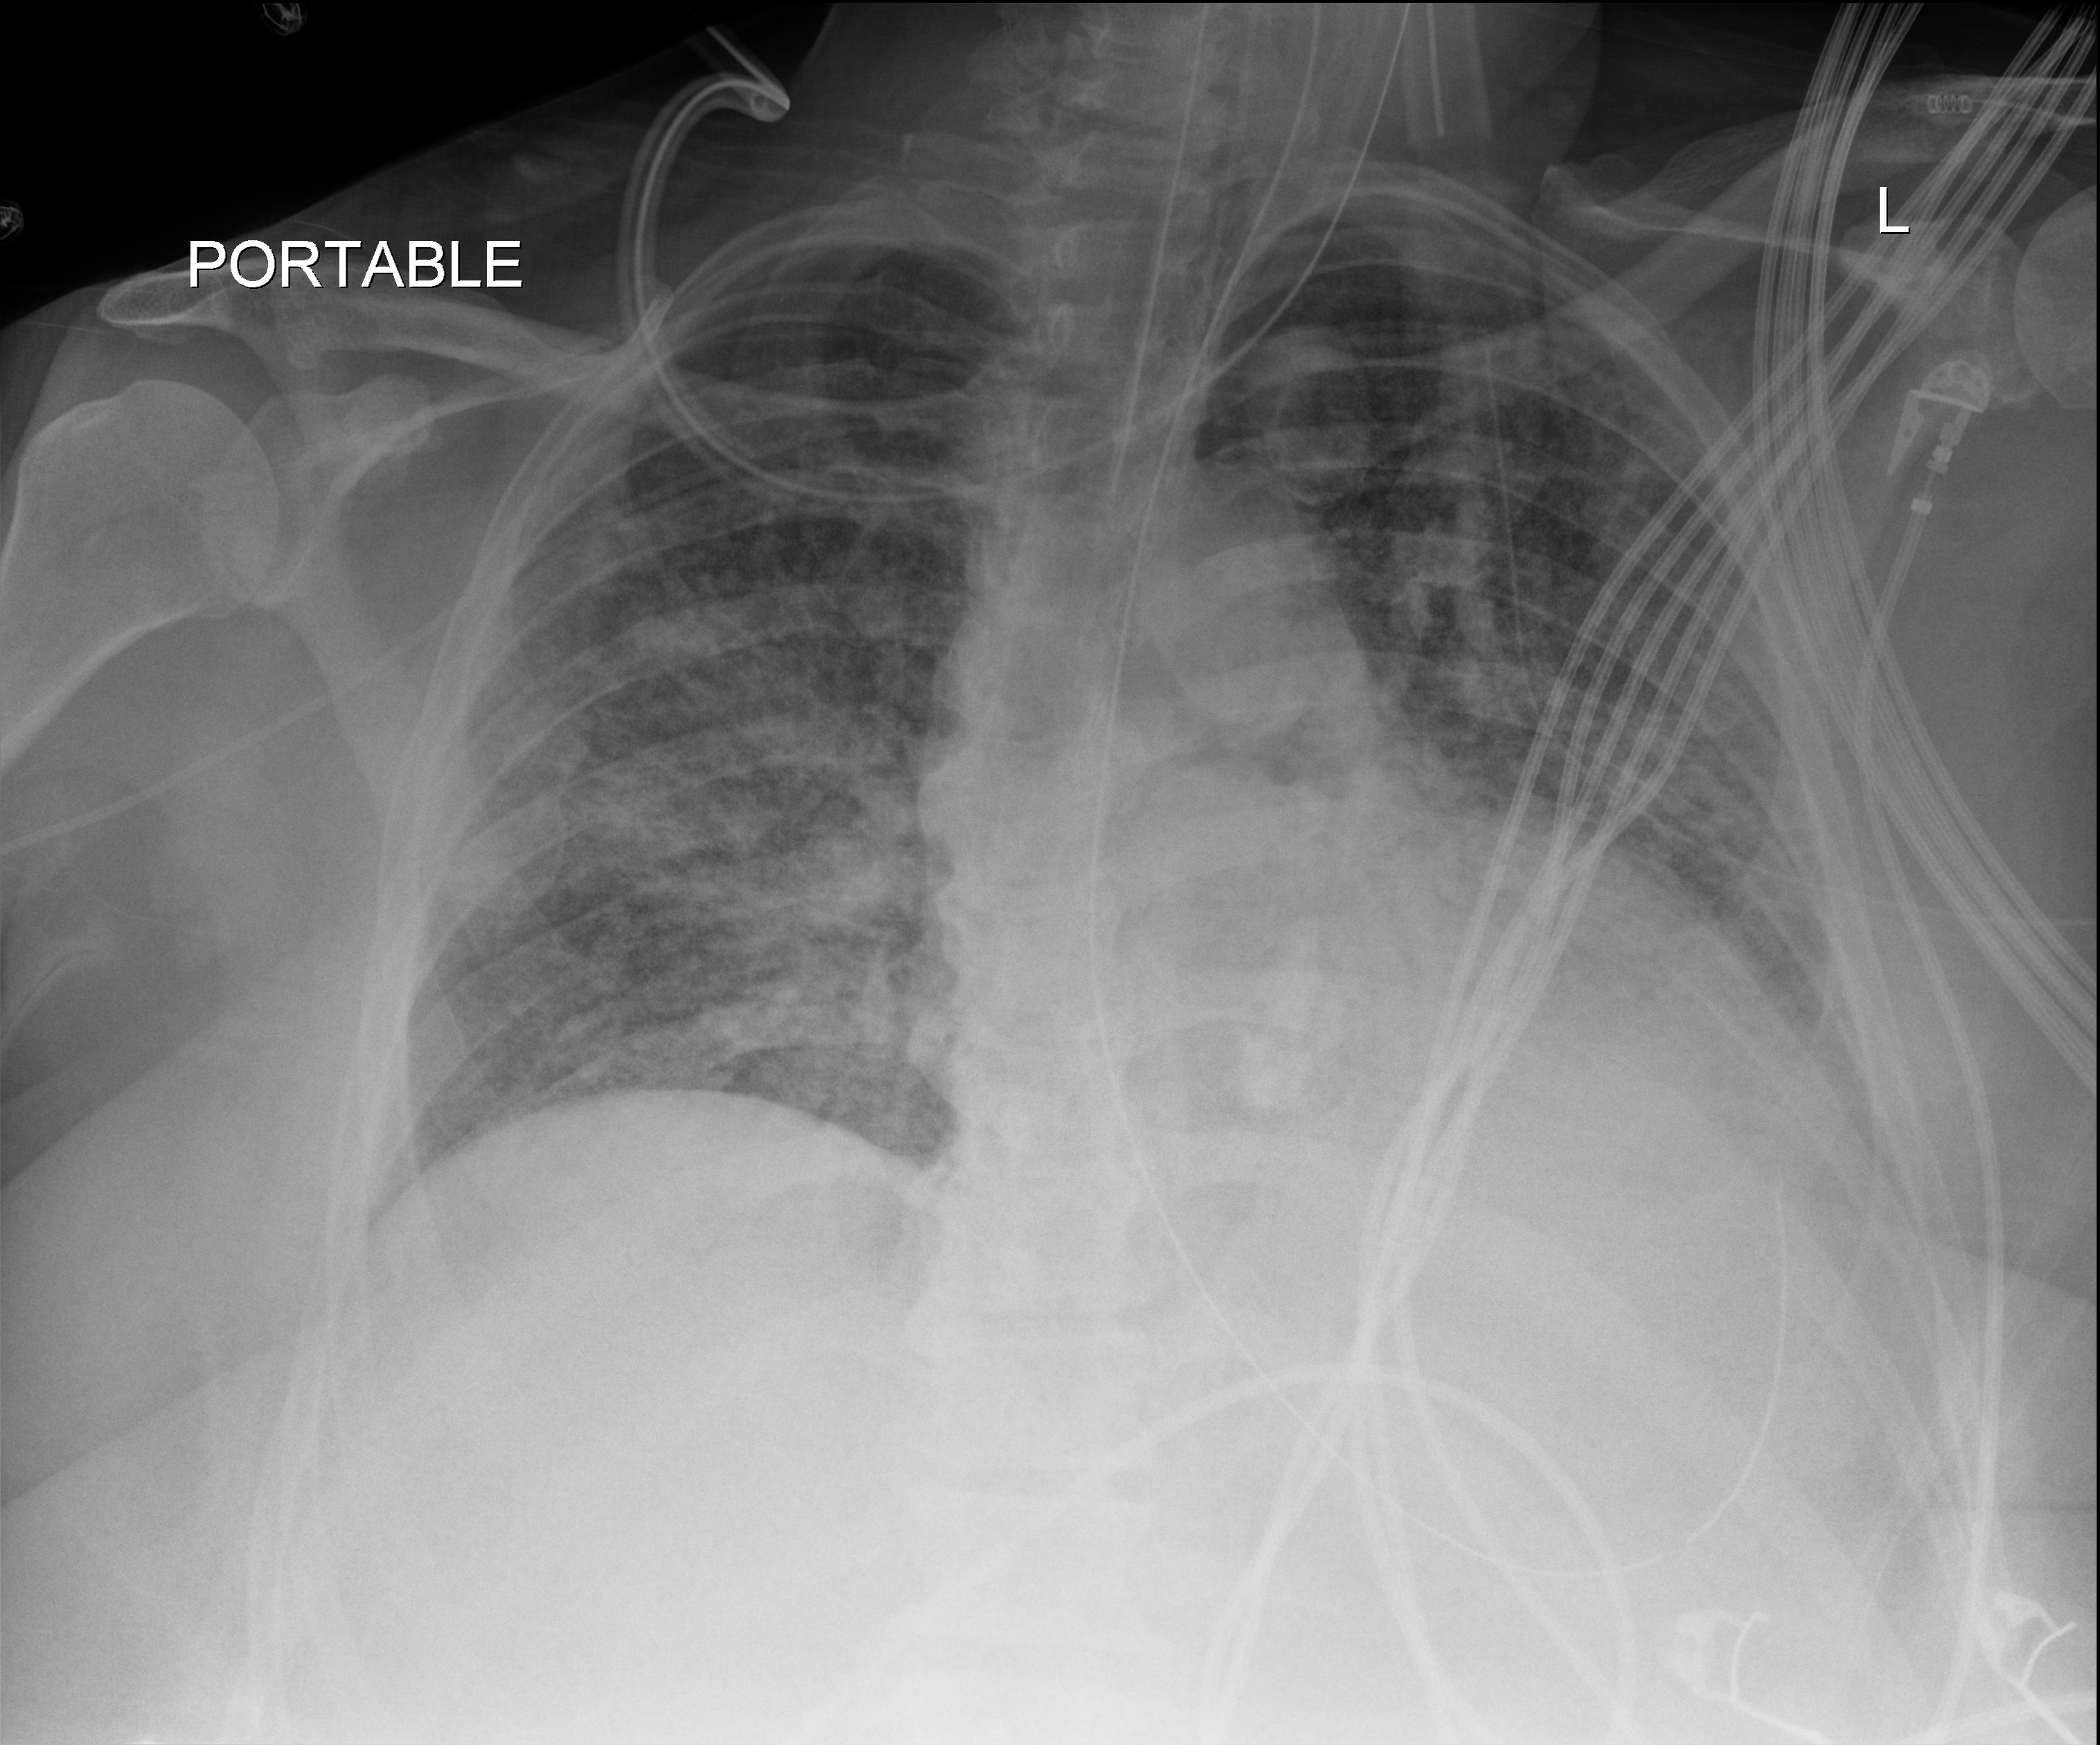
Chest X-ray, anteroposterior (AP) projection. Adult patient hospitalised with COVID-19, age 18–59 years.
Admission-level facts for this patient (not findings on this image; timing relative to this image not recorded): length of hospital stay: 28 days; mechanically ventilated during this hospital stay: yes; admitted to intensive care during this hospital stay: yes.